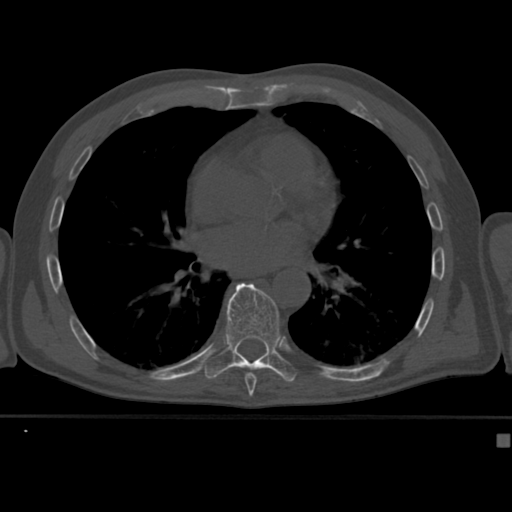
CT including the spine, one axial slice. Slice 251 of 430 in the series (ordered by position). Reconstruction kernel Br40s. Bone window (W 1800 / L 400 HU). 1.5 mm slice thickness. 512 × 512 image matrix. Patient: male, 64 years. Case-level facts recorded for this patient, not image findings: primary cancer: uterus.
Structures marked on this image (semi-automatic segmentation, software-assisted and operator-edited):
- T8 vertebra: box from (x=245, y=373) to (x=257, y=382) px
- T9 vertebra: (x=202, y=283)–(x=299, y=382)